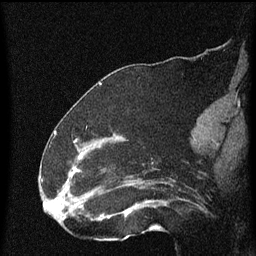
Breast MRI (dynamic contrast-enhanced), one sagittal slice. Position 30 of 60 along the scan axis. Dynamic contrast-enhanced series, image 2 of 4 at this slice position (ordered by acquisition). 1.5 T. TE 4.2 ms, TR 8 ms. 2 mm slice thickness. 256 × 256 image matrix, field of view 180 × 180 mm. Female patient, age 52 years.
Annotated regions visible in this slice (semi-automatic segmentation, software-assisted and operator-edited):
- analysis volume of interest (the breast-tissue region the enhancement analysis was run in; not a lesion): box from (x=73, y=148) to (x=172, y=219) px
- tumour enhancement mask (voxels above the 70 % enhancement threshold inside the analysis volume of interest): (x=73, y=152)–(x=152, y=219)